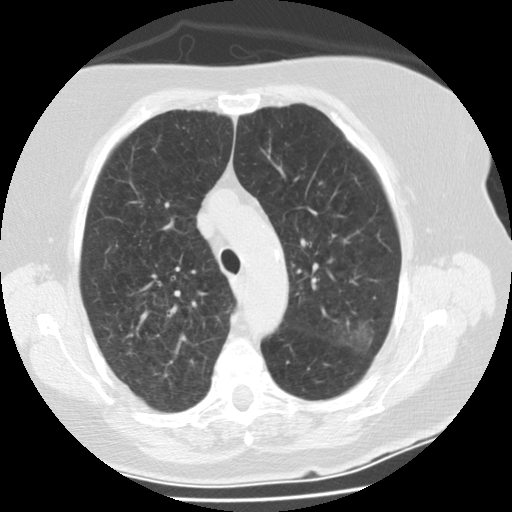
Low-dose screening chest CT, axial slice. Second screening round (one year after baseline). Lung window (W 1500 / L -600 HU). 2.5 mm slice thickness. Slice 75 of 297 in the series. 512 × 512 image matrix, field of view 321 × 321 mm. Female, age 74 years at enrolment. Former smoker at enrolment.
Expert-annotated lung lesion, bounding box [x1, y1, x2, y2] px = [328, 310, 386, 362]. The screening reader recorded 3 non-calcified nodules or masses ≥4 mm on this exam (right lower lobe, left upper lobe, left upper lobe); which of them this box marks is not recorded. Official screen result: positive, other. Participant outcome: lung cancer diagnosed 68 days after this screen — bronchiolo-alveolar adenocarcinoma, NOS, left upper lobe, stage IA (AJCC 6th edition), 20 mm at pathology.